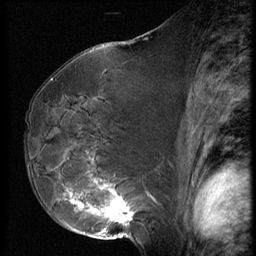
Breast MRI (dynamic contrast-enhanced), one sagittal slice. Position 36 of 62 along the scan axis. 3 images stored at this slice position (order not interpretable as contrast timing). 1.5 T. TE 4.2 ms, TR 9 ms. 2.5 mm slice thickness. 256 × 256 image matrix, field of view 180 × 180 mm. Patient: female, 50 years. From the clinical record (not read from this slice): setting: breast cancer imaged before/during neoadjuvant chemotherapy; receptor status: HR-positive, HER2-negative.
Annotated regions visible in this slice (semi-automatically segmented with operator editing):
- analysis volume of interest (the breast-tissue region the enhancement analysis was run in; not a lesion): bounding box (x1, y1, x2, y2) in pixels: (59, 125, 139, 238)
- tumour enhancement mask (voxels above the 140 % enhancement threshold inside the analysis volume of interest): (59, 190, 136, 231)